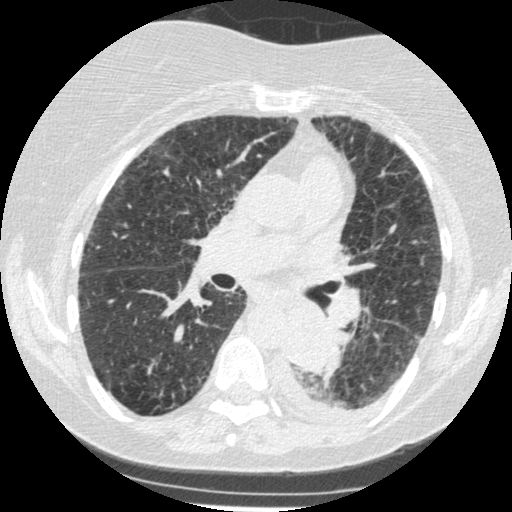
Chest CT (low-dose screening protocol), one axial image; third screening round (two years after baseline); lung window (W 1500 / L -600 HU); slice 201 of 341 in the series. Female, age 60 years at enrolment. Former smoker at enrolment.
- Expert reader's lesion annotation, bounding box <271,307,342,374> (left, top, right, bottom; pixels).
- The exam's reader record, not a measurement of the box and not confirmed to be the same lesion: non-calcified nodule or mass ≥4 mm, left lower lobe, 54 × 38 mm, smooth margins, soft tissue attenuation, pre-existing on the prior screen: yes; interval growth: yes.
- Participant outcome: lung cancer diagnosed 15 days after this screen — small cell carcinoma, NOS, left lower lobe, undifferentiated (G4), stage IV (AJCC 6th edition), 69 mm at pathology.